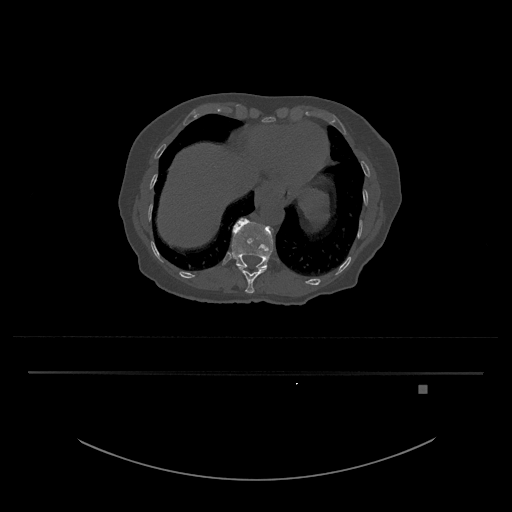
CT including the spine, one axial slice; slice 638 of 797 in the series (ordered by position); reconstruction kernel Br40s/3; 120 kVp; bone window (W 1800 / L 400 HU); 512 × 512 image matrix, field of view 500 × 500 mm. Patient: female, 57 years. Case-level facts recorded for this patient, not image findings: primary cancer: cervical.
Annotated regions visible in this slice (semi-automatically segmented with operator editing):
- T11 vertebra: bounding box (x1, y1, x2, y2) in pixels: (238, 266, 267, 293)
- T12 vertebra: (231, 218, 273, 269)